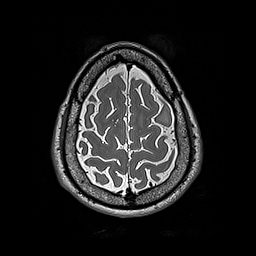
Brain MRI from a brain-tumour surgery series, one axial slice; position 54 of 192 along the scan axis; 1 mm slice thickness; 256 × 256 image matrix. From the clinical record (not read from this slice): histopathology: Astrocytoma; WHO grade: 2; IDH mutation: yes.
Structures marked on this image (manually delineated by an expert):
- tumour: box from (x=157, y=108) to (x=169, y=125) px